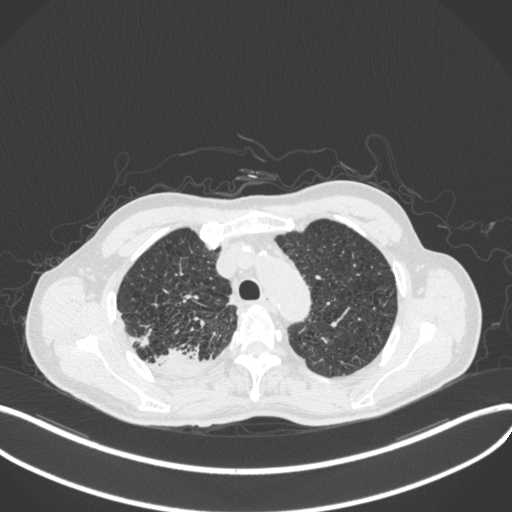
Chest CT, one axial slice. Slice 346 of 423 in the series (ordered by position). Reconstruction kernel B31f. 120 kVp. Lung window (W 1500 / L -600 HU). 512 × 512 image matrix, field of view 400 × 400 mm. Male patient, age 79 years. Case-level facts recorded for this patient, not image findings: clinical TNM (as recorded): T3 N0 M0.
Outlined on this slice (rectangle marked by the reading radiologist):
- lung tumour (recorded histology: adenocarcinoma): box from (x=149, y=343) to (x=211, y=378) px